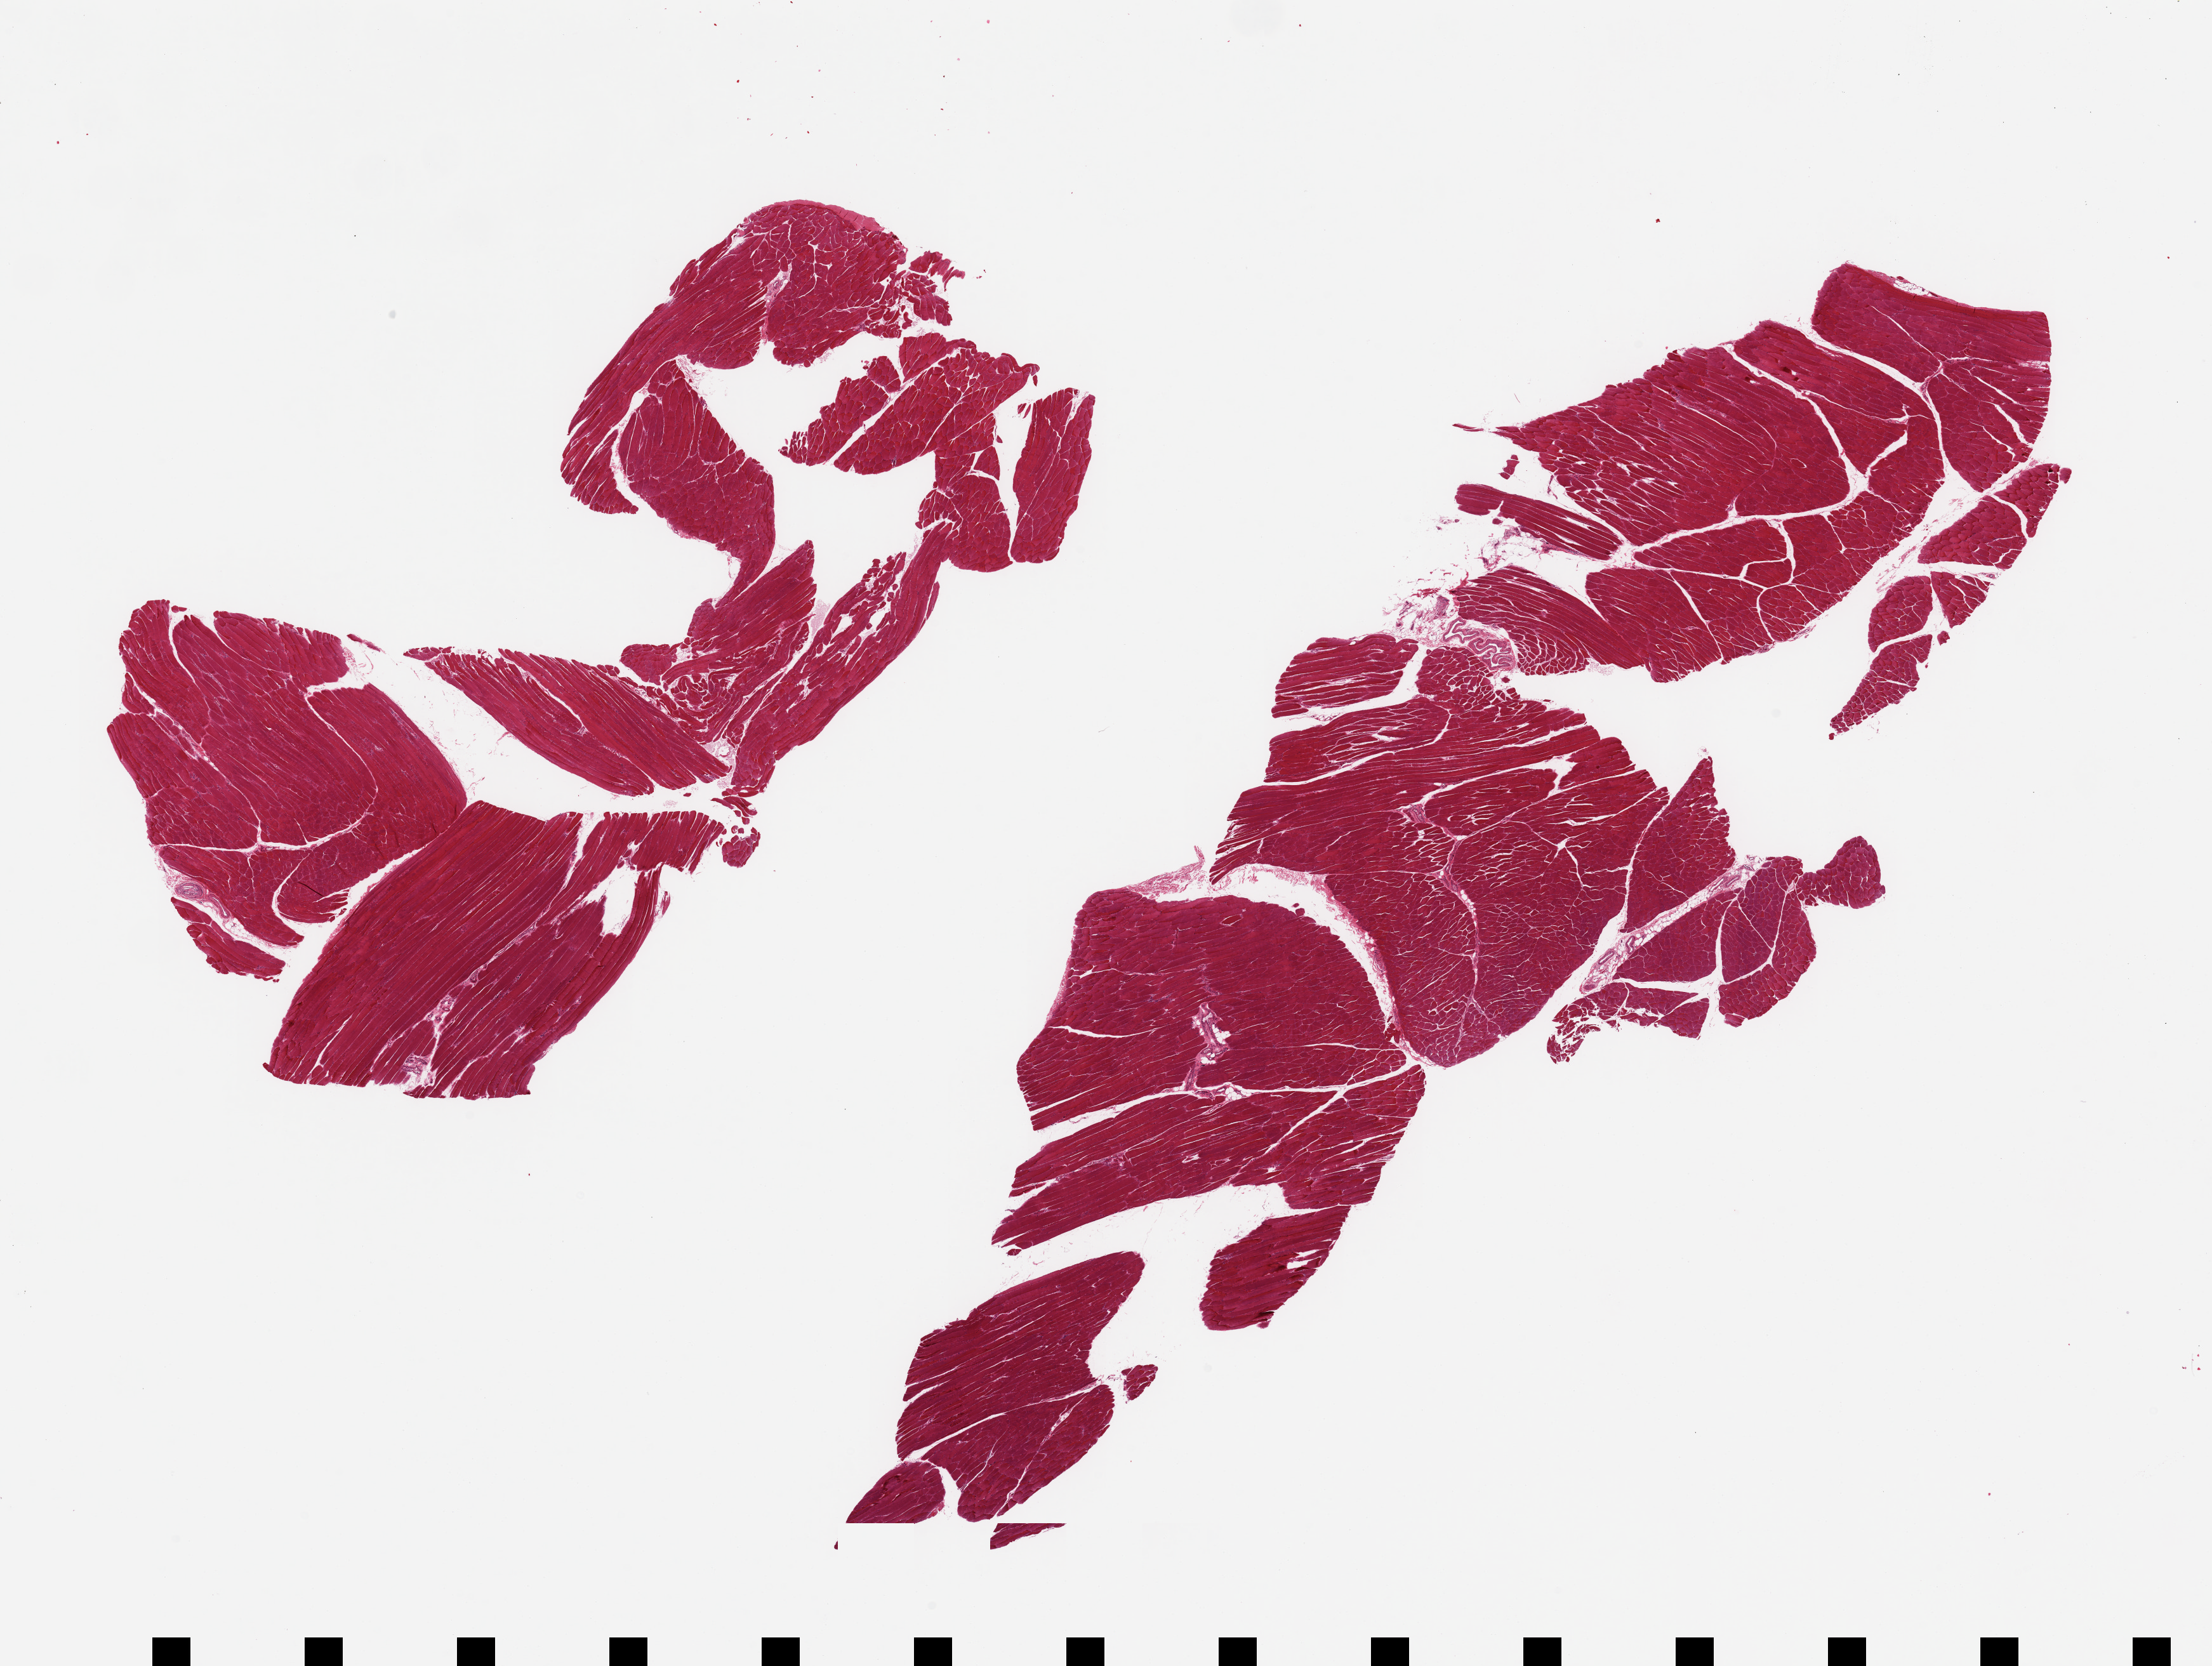
H&E whole-slide image — low-resolution overview of the scanned area, about 27.6 x 20.8 mm (acquisition: 20x scan), PAXgene-fixed, paraffin-embedded tissue, section of skeletal muscle (target tissue), tissue donor sample.
Reviewer comment on this tissue sample: 2 fragmented pieces; 5% internal fat.